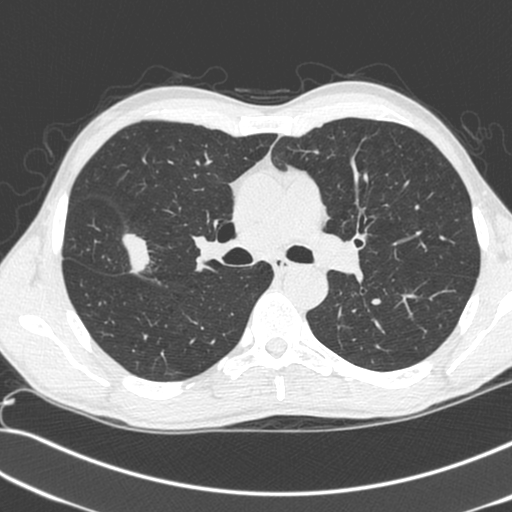
Axial slice from a low-dose chest CT screening exam, first (baseline) screen, lung window (W 1500 / L -600 HU), standard (soft-tissue) reconstruction kernel (C). Male, age 55 years at enrolment.
Lesion marked by an expert reader, box from (x=66, y=215) to (x=159, y=294) px. The exam's reader record, not a measurement of the box and not confirmed to be the same lesion: non-calcified nodule or mass ≥4 mm, right upper lobe, 52 × 39 mm, spiculated (stellate) margins, soft tissue attenuation. Lung cancer was diagnosed 25 days after this screen: large cell neuroendocrine carcinoma, right upper lobe, poorly differentiated (G3), stage IIB (AJCC 6th edition), 49 mm at pathology.